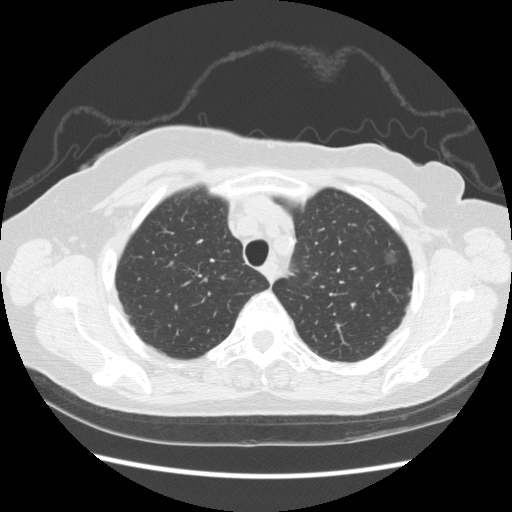
Axial slice from a low-dose chest CT screening exam. First (baseline) screen. Lung window (W 1500 / L -600 HU). Slice 37 of 247 in the series. Female, age 73 years at enrolment. Former smoker at enrolment.
Expert reader's lesion annotation, bounding box [x1, y1, x2, y2] px = [373, 229, 416, 274]. The screening reader recorded 3 non-calcified nodules or masses ≥4 mm on this exam (left upper lobe, left upper lobe, left upper lobe); which of them this box marks is not recorded. Later outcome: lung cancer diagnosed 445 days after this screen — bronchiolo-alveolar adenocarcinoma, NOS, left upper lobe, well differentiated (G1), stage IA (AJCC 6th edition), 10 mm at pathology.